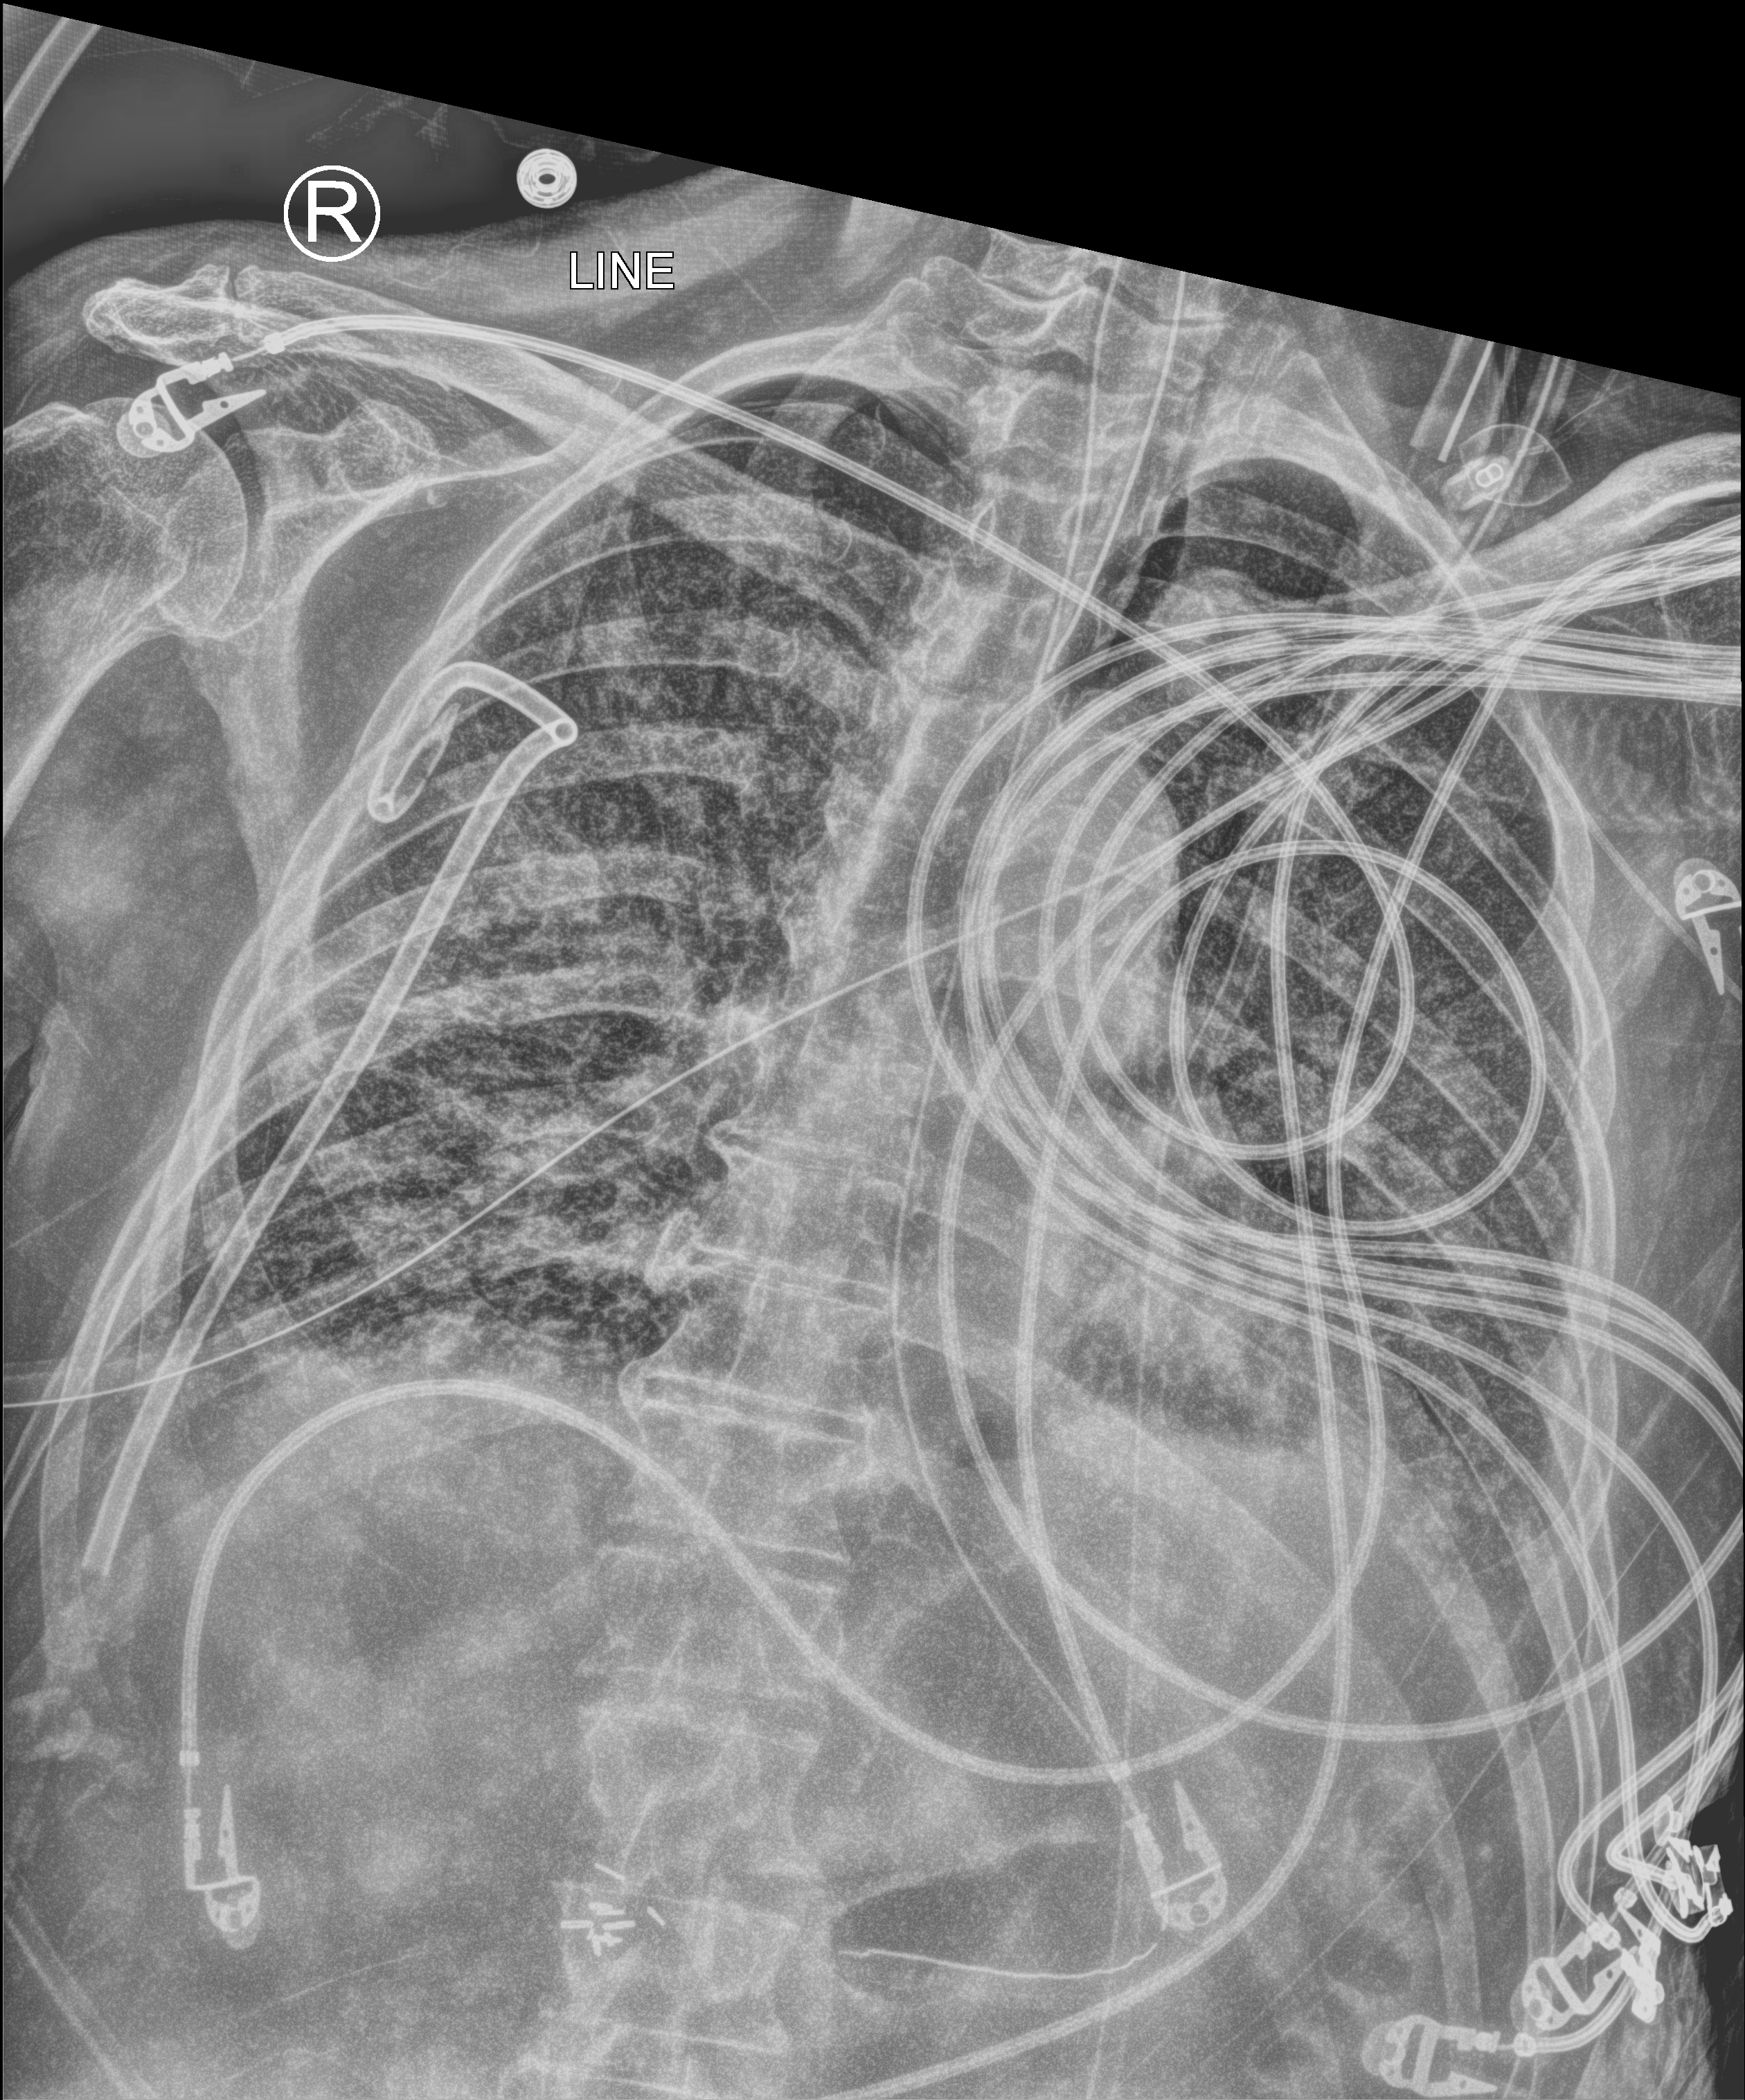
Bedside chest radiograph (computed radiography), anteroposterior (AP) projection. Male patient hospitalised with COVID-19, age 75–90 years.
Hospital-stay facts (about this admission, not read from this image; timing relative to this image not recorded): admitted to intensive care during this hospital stay: yes; diabetes (admission record): no; mechanically ventilated during this hospital stay: yes.